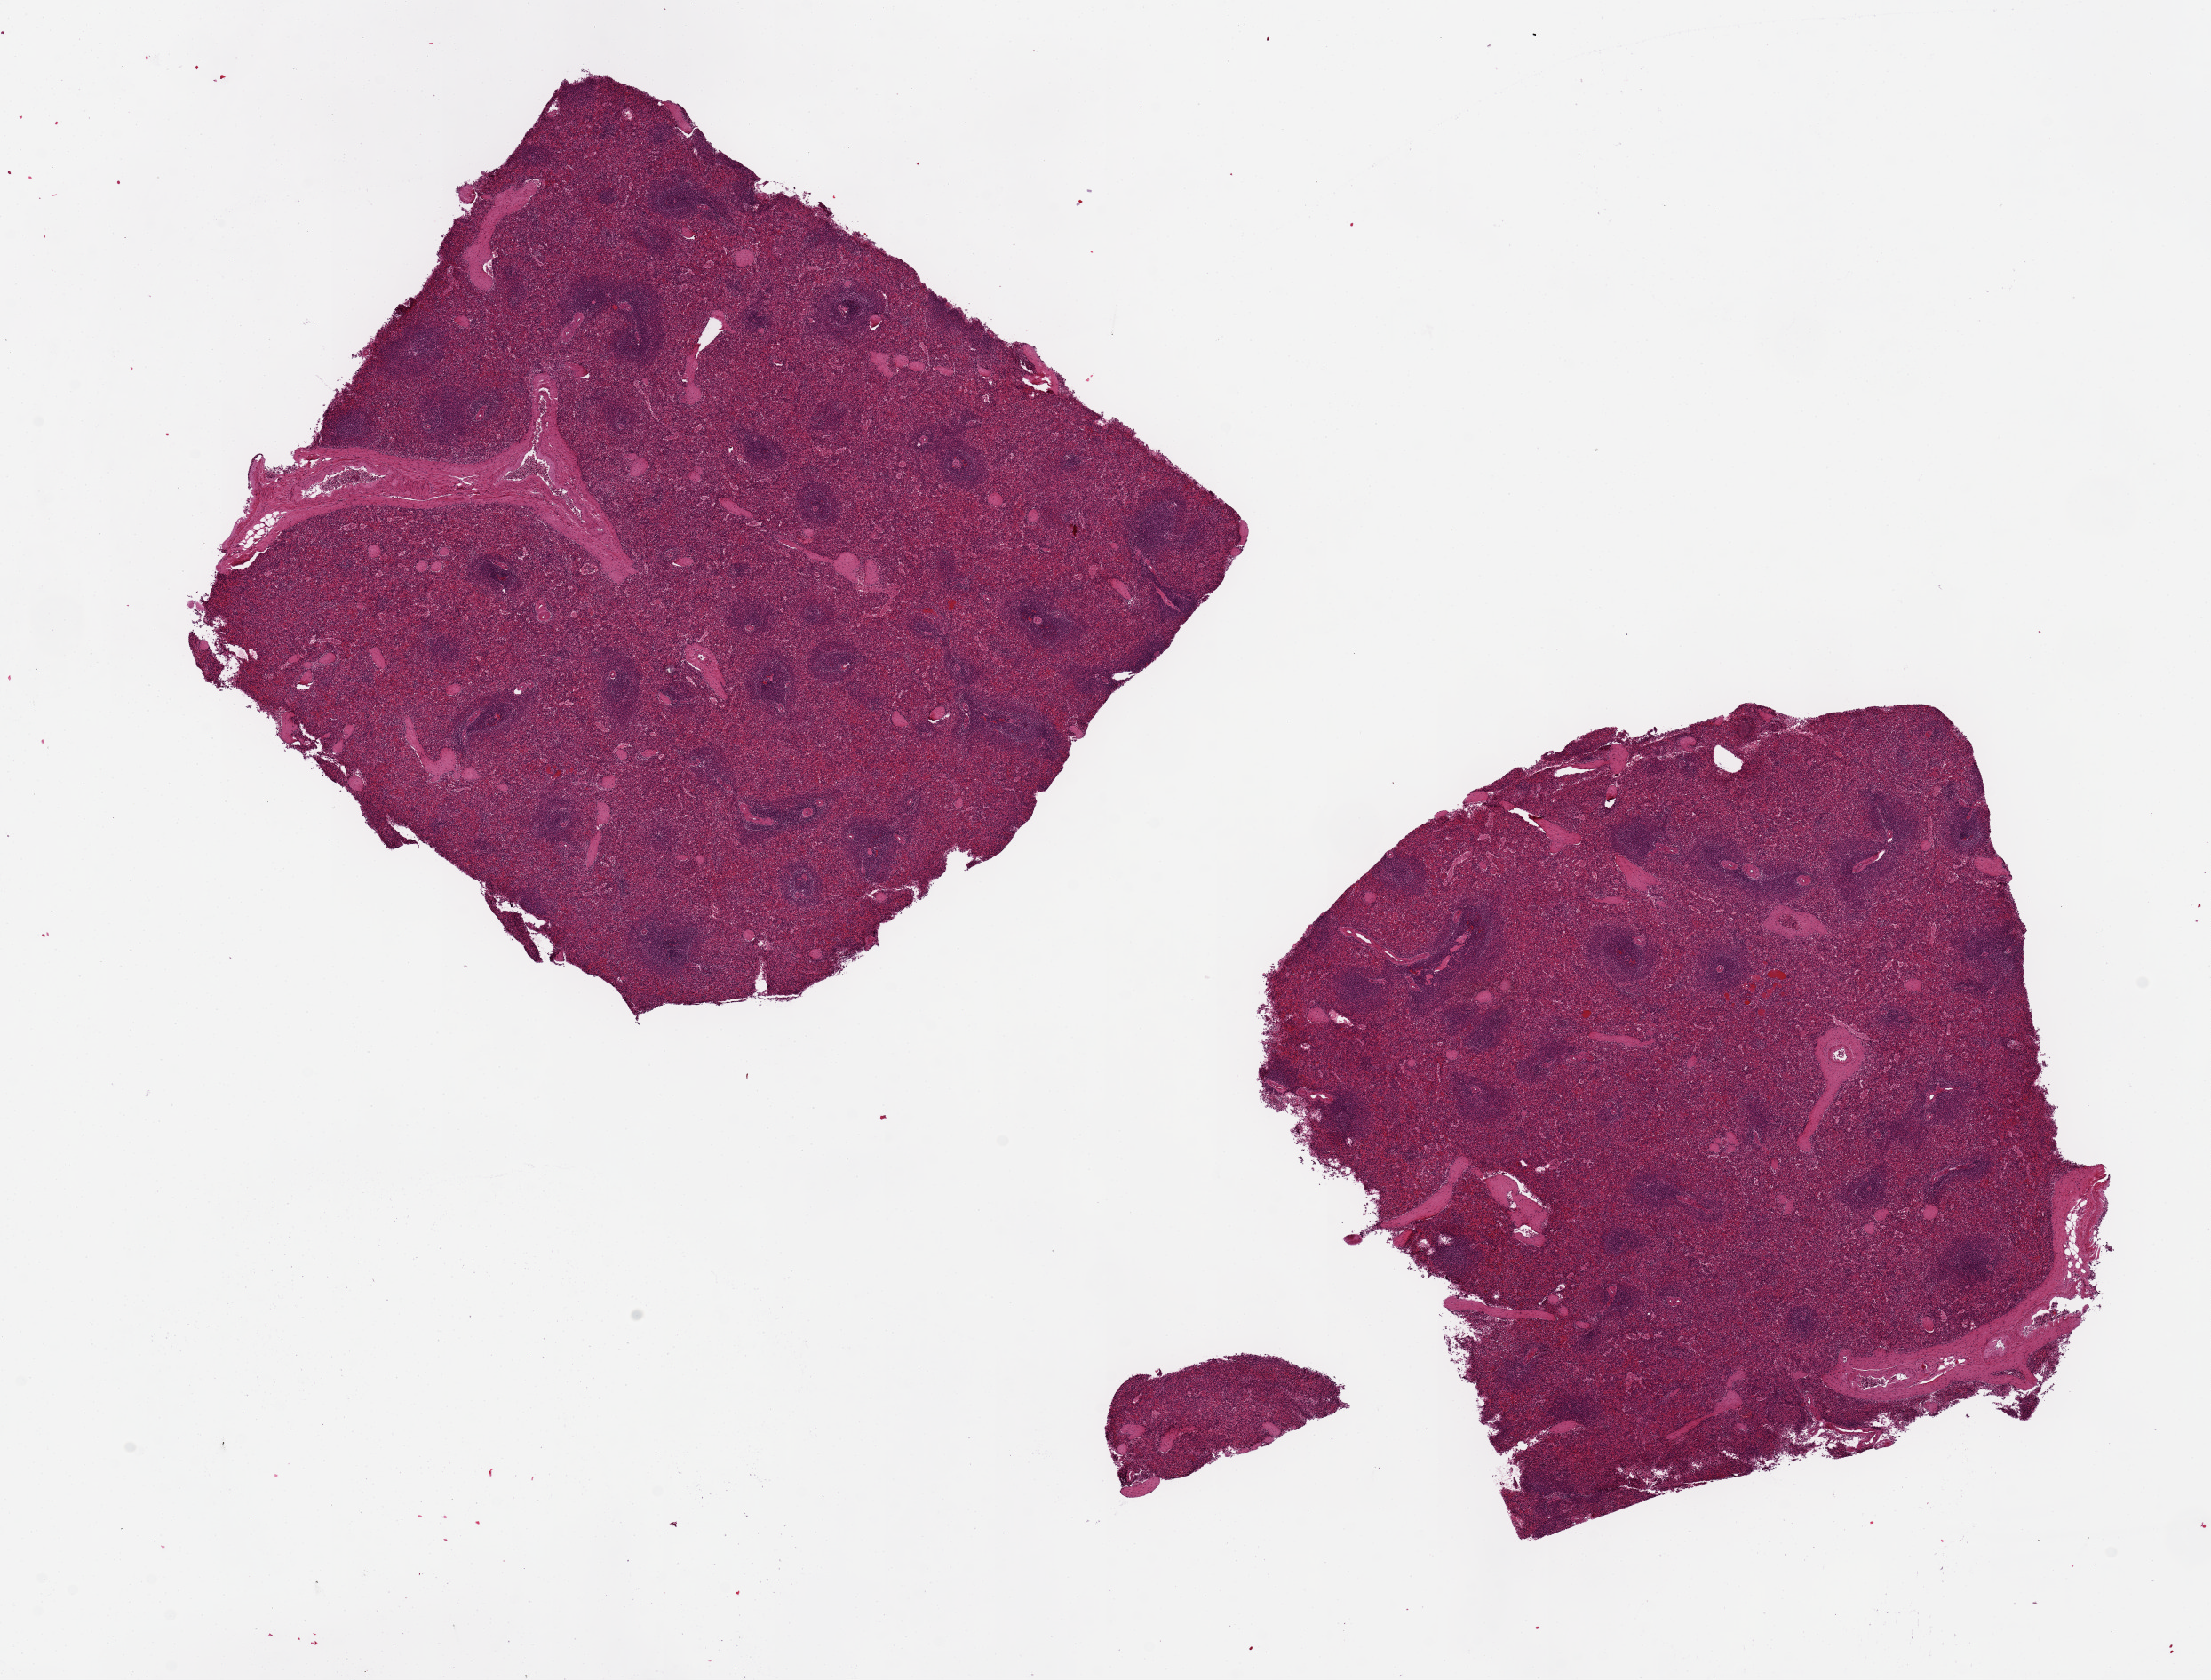
Whole-slide image, hematoxylin and eosin (H&E) stain, whole scanned area (about 19.7 x 15.0 mm, acquisition: 20x scan) shown as a low-resolution overview. PAXgene-fixed, paraffin-embedded tissue. Section of spleen (target tissue). Donor tissue sample. Donor: male.
Reviewer comment on this tissue sample: 2 pieces both 6.5x7 mm; little congestion.